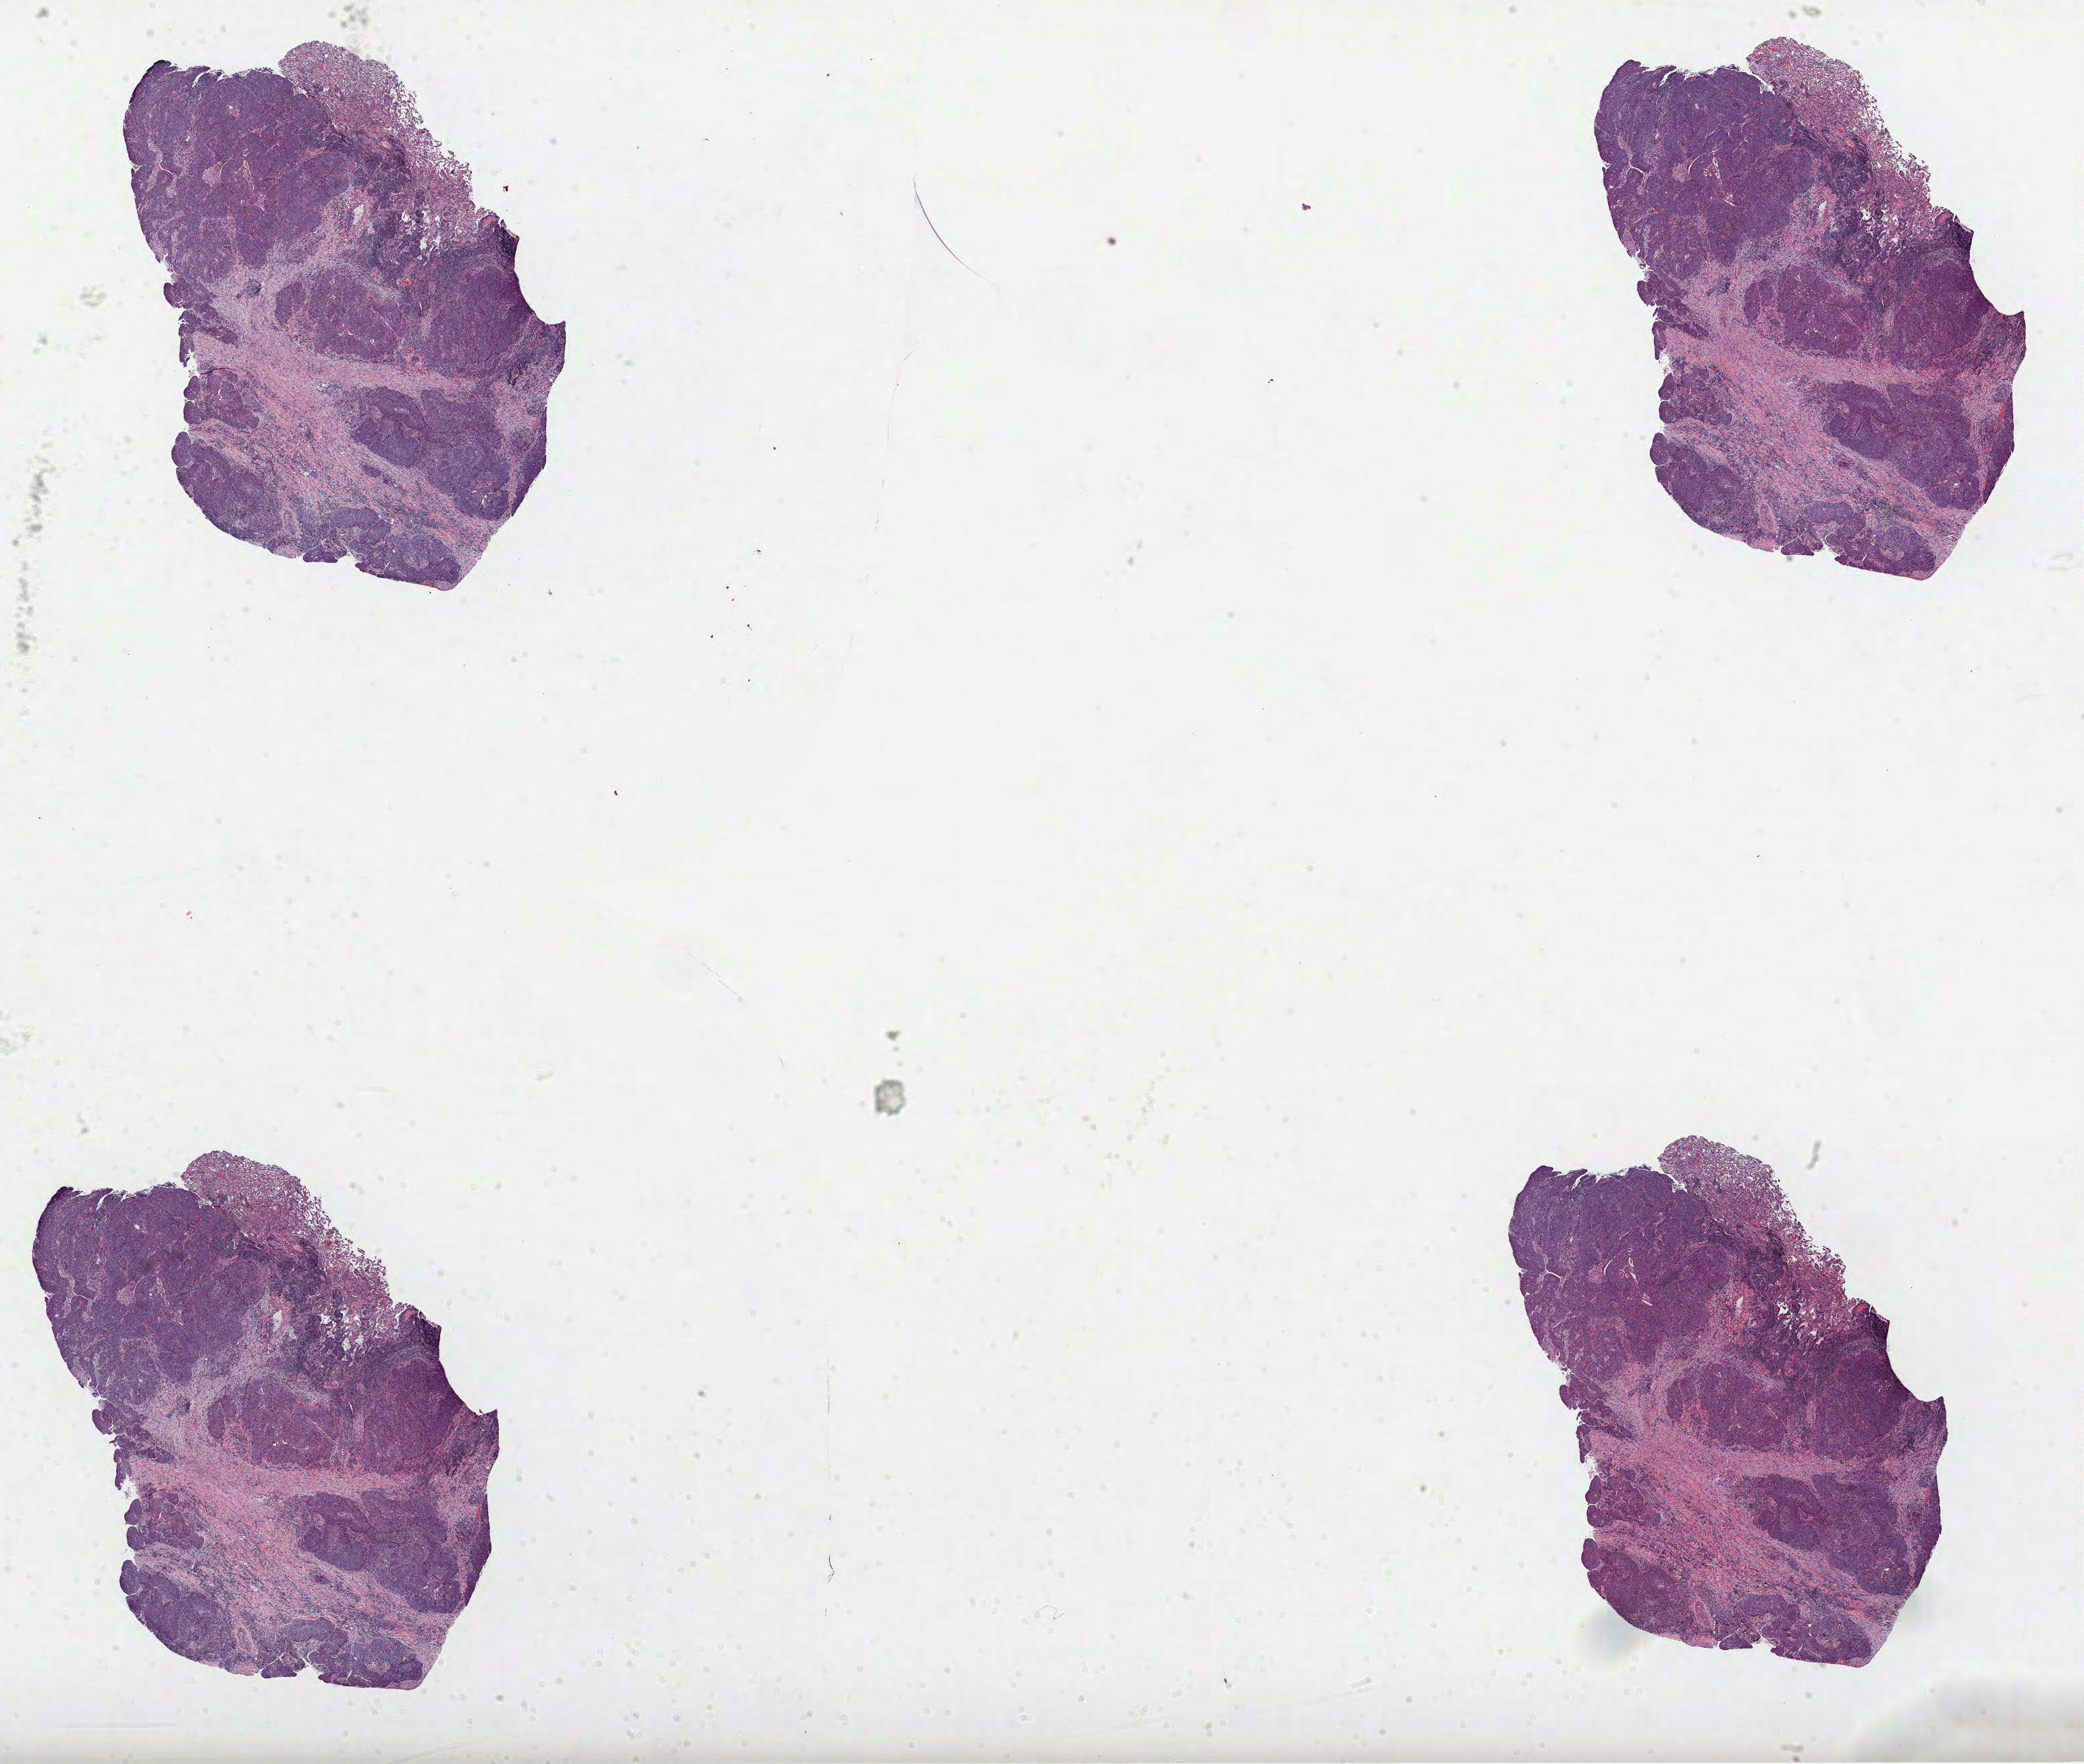
Whole-slide histology image, Hematoxylin and eosin (H&E) stained — low-resolution overview of the scanned area, about 24.9 x 21.1 mm, formalin-fixed paraffin-embedded (FFPE) diagnostic section, lung, primary tumour sample. Patient: male, age at initial diagnosis 53 years.
• AJCC pathologic stage: IIIA
• histologic diagnosis: Adenocarcinoma, NOS (lower lobe, lung)